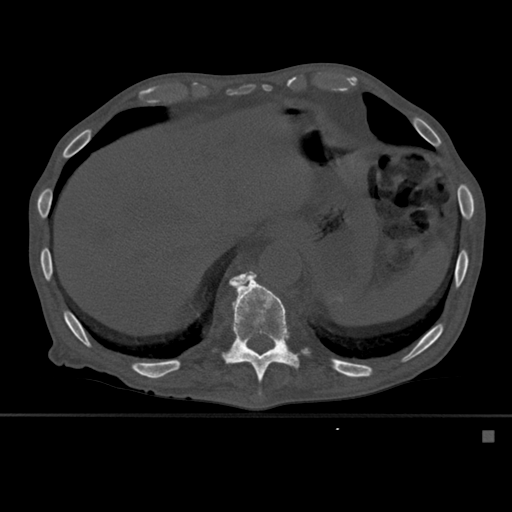
CT including the spine, one axial slice. Position 297 of 527 along the scan axis. Bone window (W 1800 / L 400 HU). 512 × 512 image matrix, field of view 373 × 373 mm. Patient: male, 78 years. From the clinical record (not read from this slice): primary cancer: prostate.
Outlined on this slice (semi-automatically segmented with operator editing):
- T10 vertebra: box from (x=240, y=275) to (x=261, y=396) px
- T11 vertebra: (x=222, y=271)–(x=310, y=383)